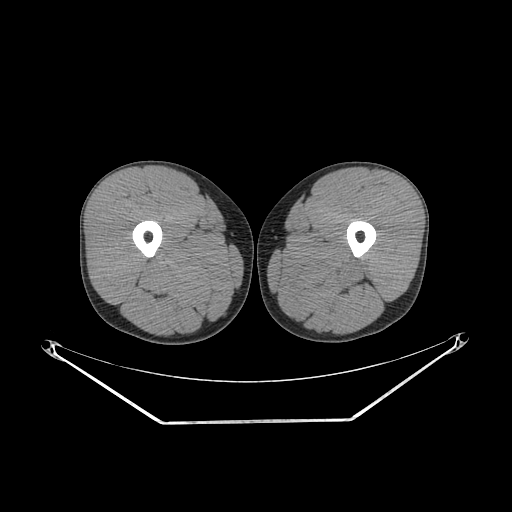
CT of an extremity soft-tissue mass (from a PET/CT study), one axial slice. Slice 232 of 267 in the series (ordered by position). Reconstruction kernel SOFT. Soft-tissue window (W 400 / L 40 HU). 512 × 512 image matrix, field of view 500 × 500 mm. Male patient. From the clinical record (not read from this slice): histological type: extraskeletal osteosarcoma; grade: high; site of the primary tumour: left adductur.
Outlined on this slice (expert contour drawn on MRI and transferred to this co-registered scan by the dataset authors):
- gross tumour volume (mass): bounding box [x1, y1, x2, y2] px = [272, 242, 371, 305]